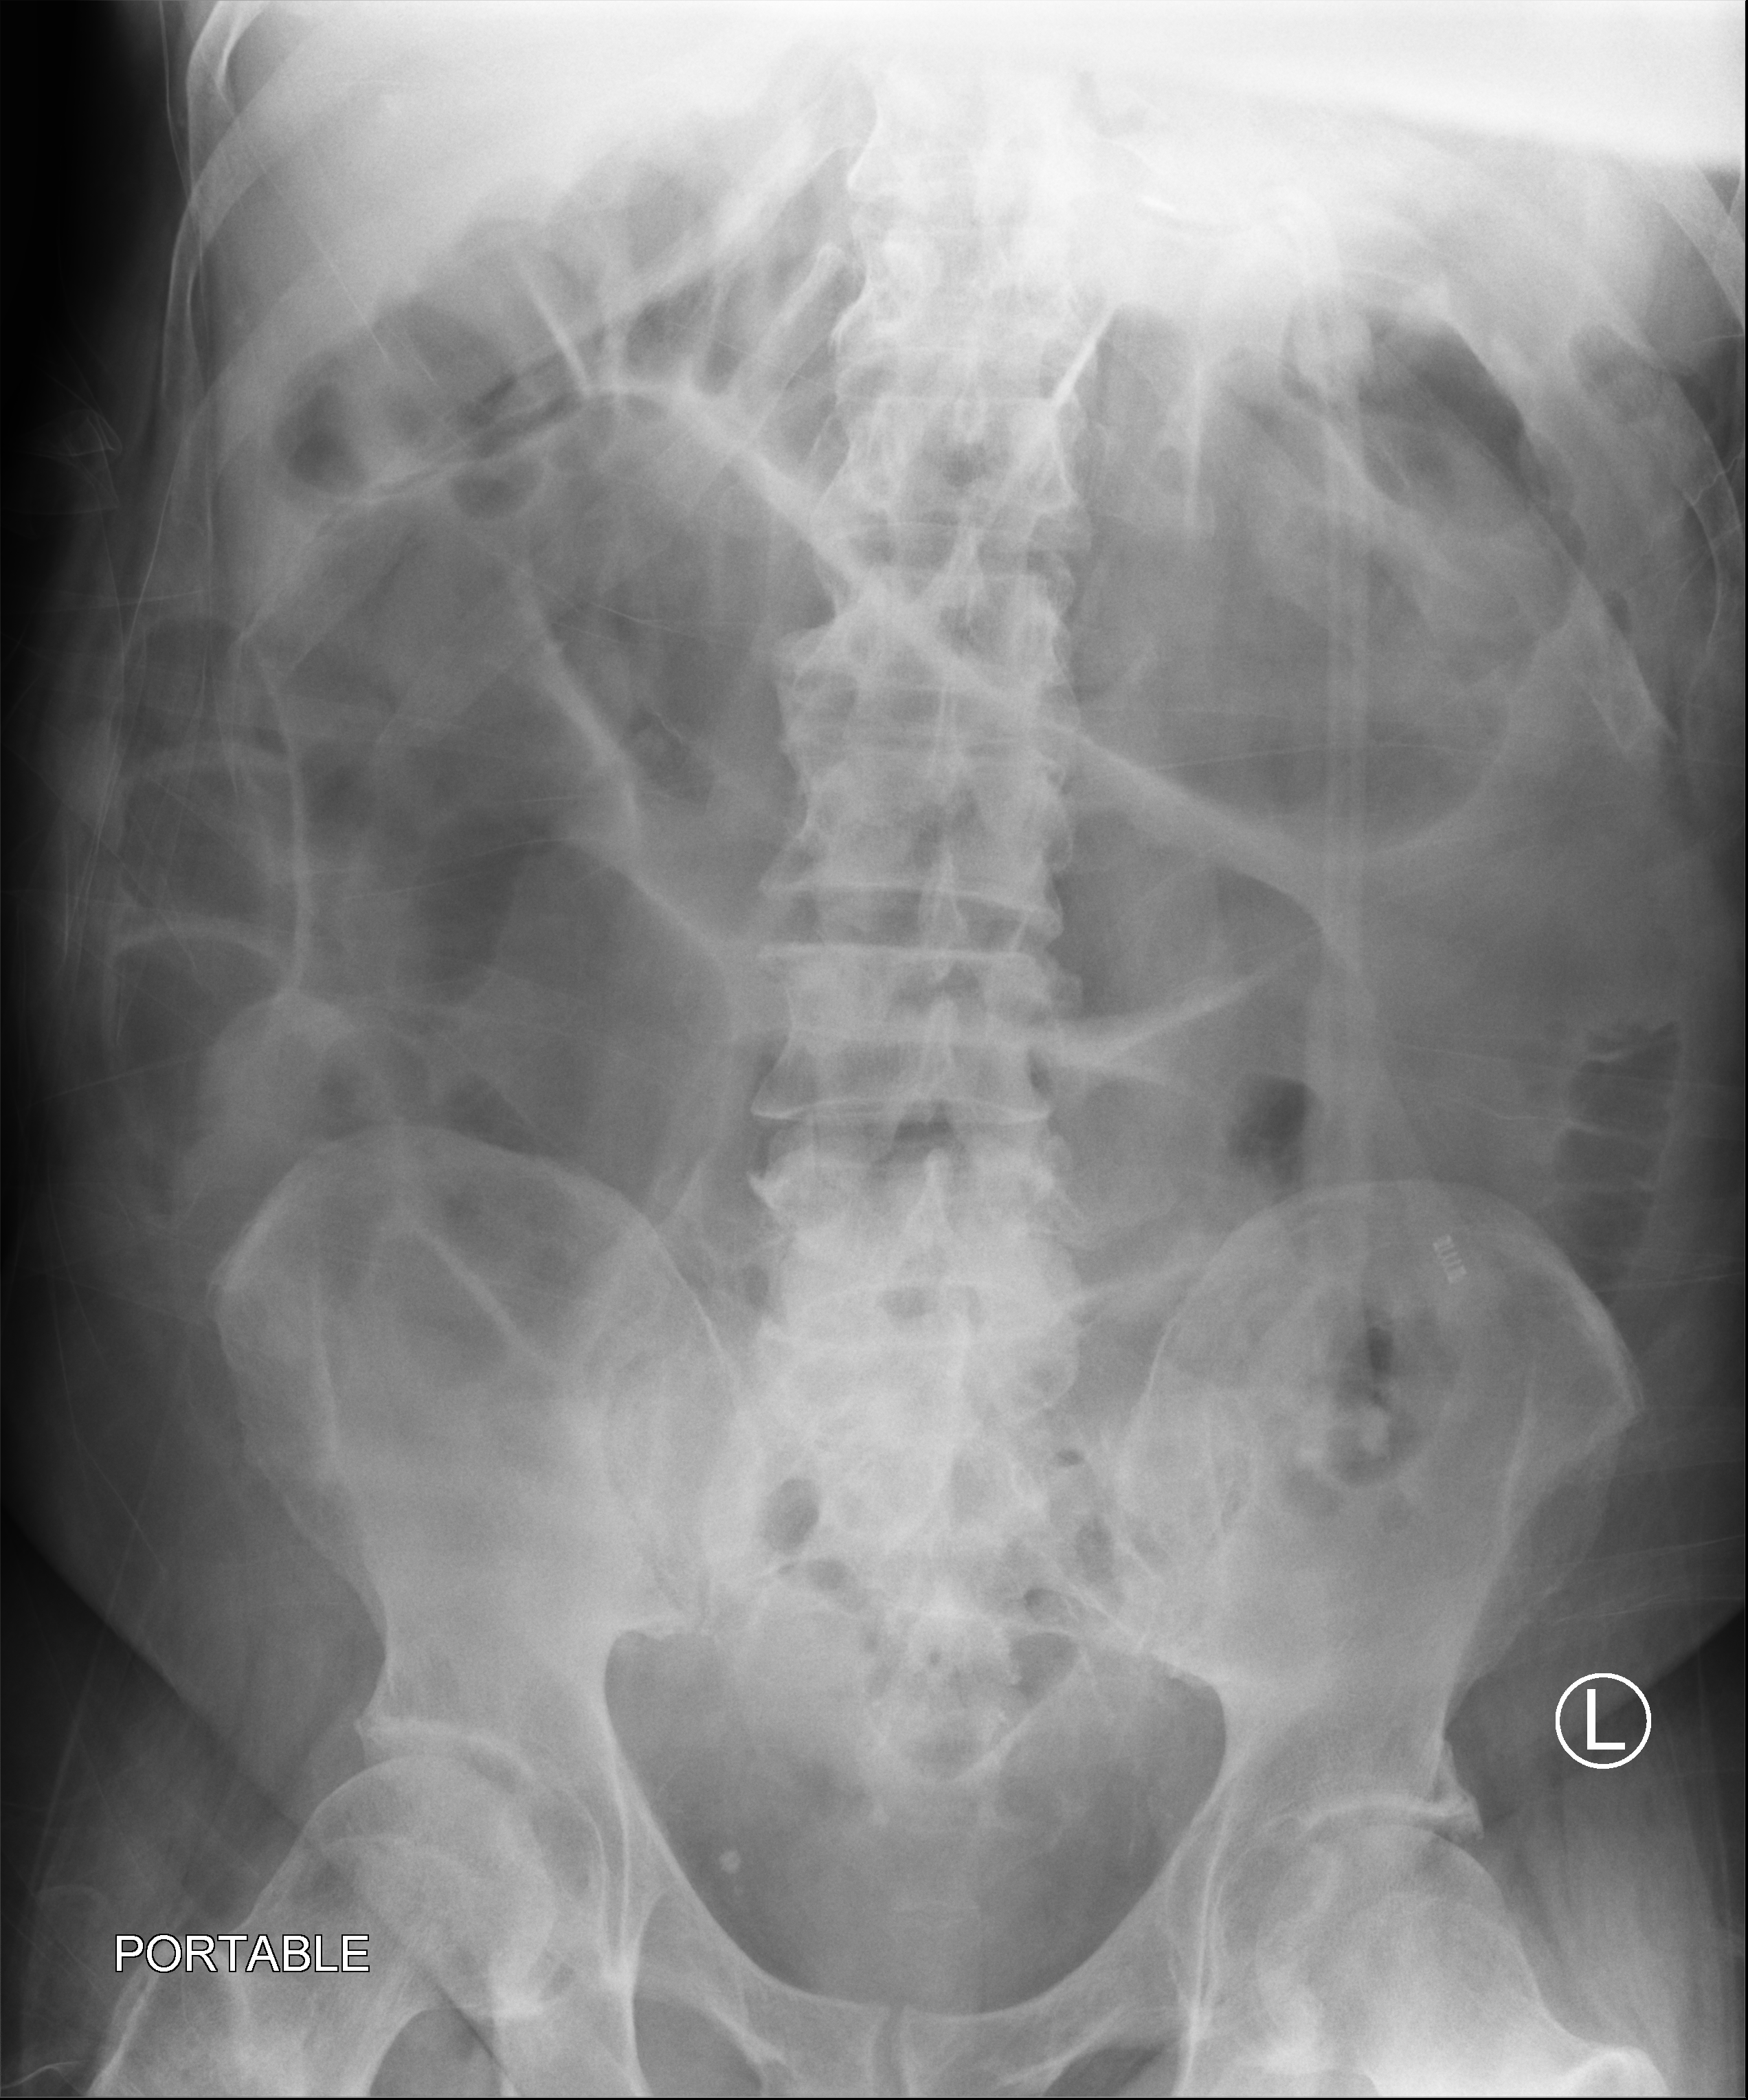
Abdomen X-ray (portable); anteroposterior (AP) projection. Patient hospitalised with COVID-19; male, aged 60–74 years.
From the hospital-stay record, not from the radiograph (when in the stay this image was taken is not recorded):
- hypertension (admission record): yes
- admitted to intensive care during this hospital stay: no
- mechanically ventilated during this hospital stay: no